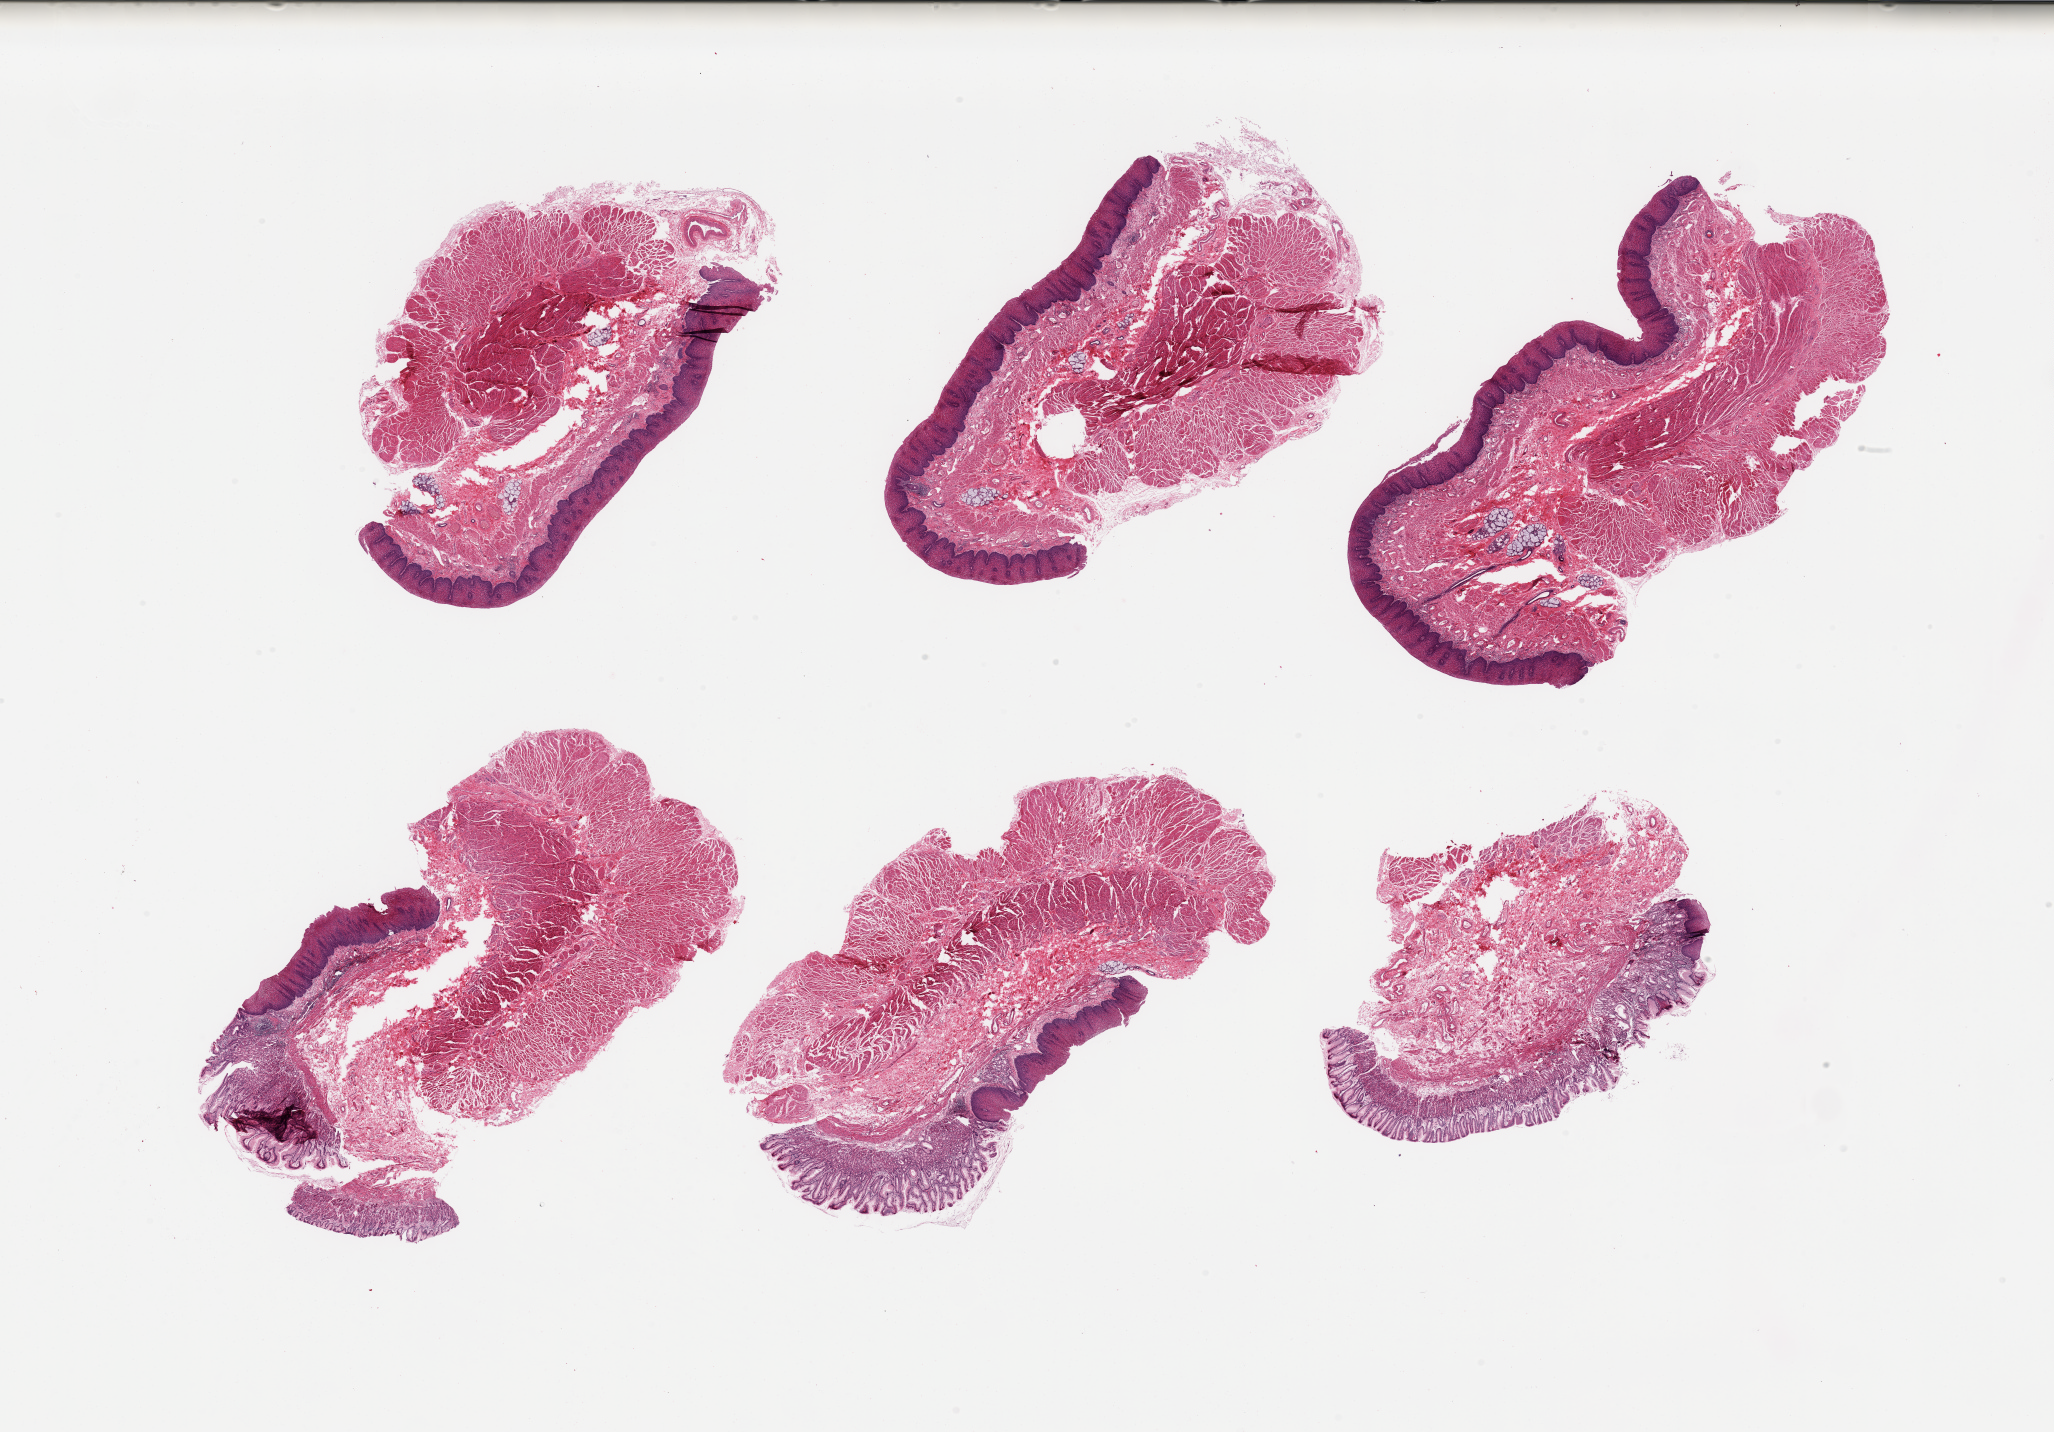
Haematoxylin and eosin whole-slide image, whole scanned area (about 32.5 x 22.6 mm, slide scanned at 20x) shown as a low-resolution overview. PAXgene-fixed paraffin-embedded (PFPE) section. Sampled site (target tissue): gastroesophageal junction. Tissue donor sample. Donor sex: female.
Pathologist's review note for this sample: 6 pieces, target muscularis is ~60% of tissue, rest is 'contaminant' mucosa/serosa.